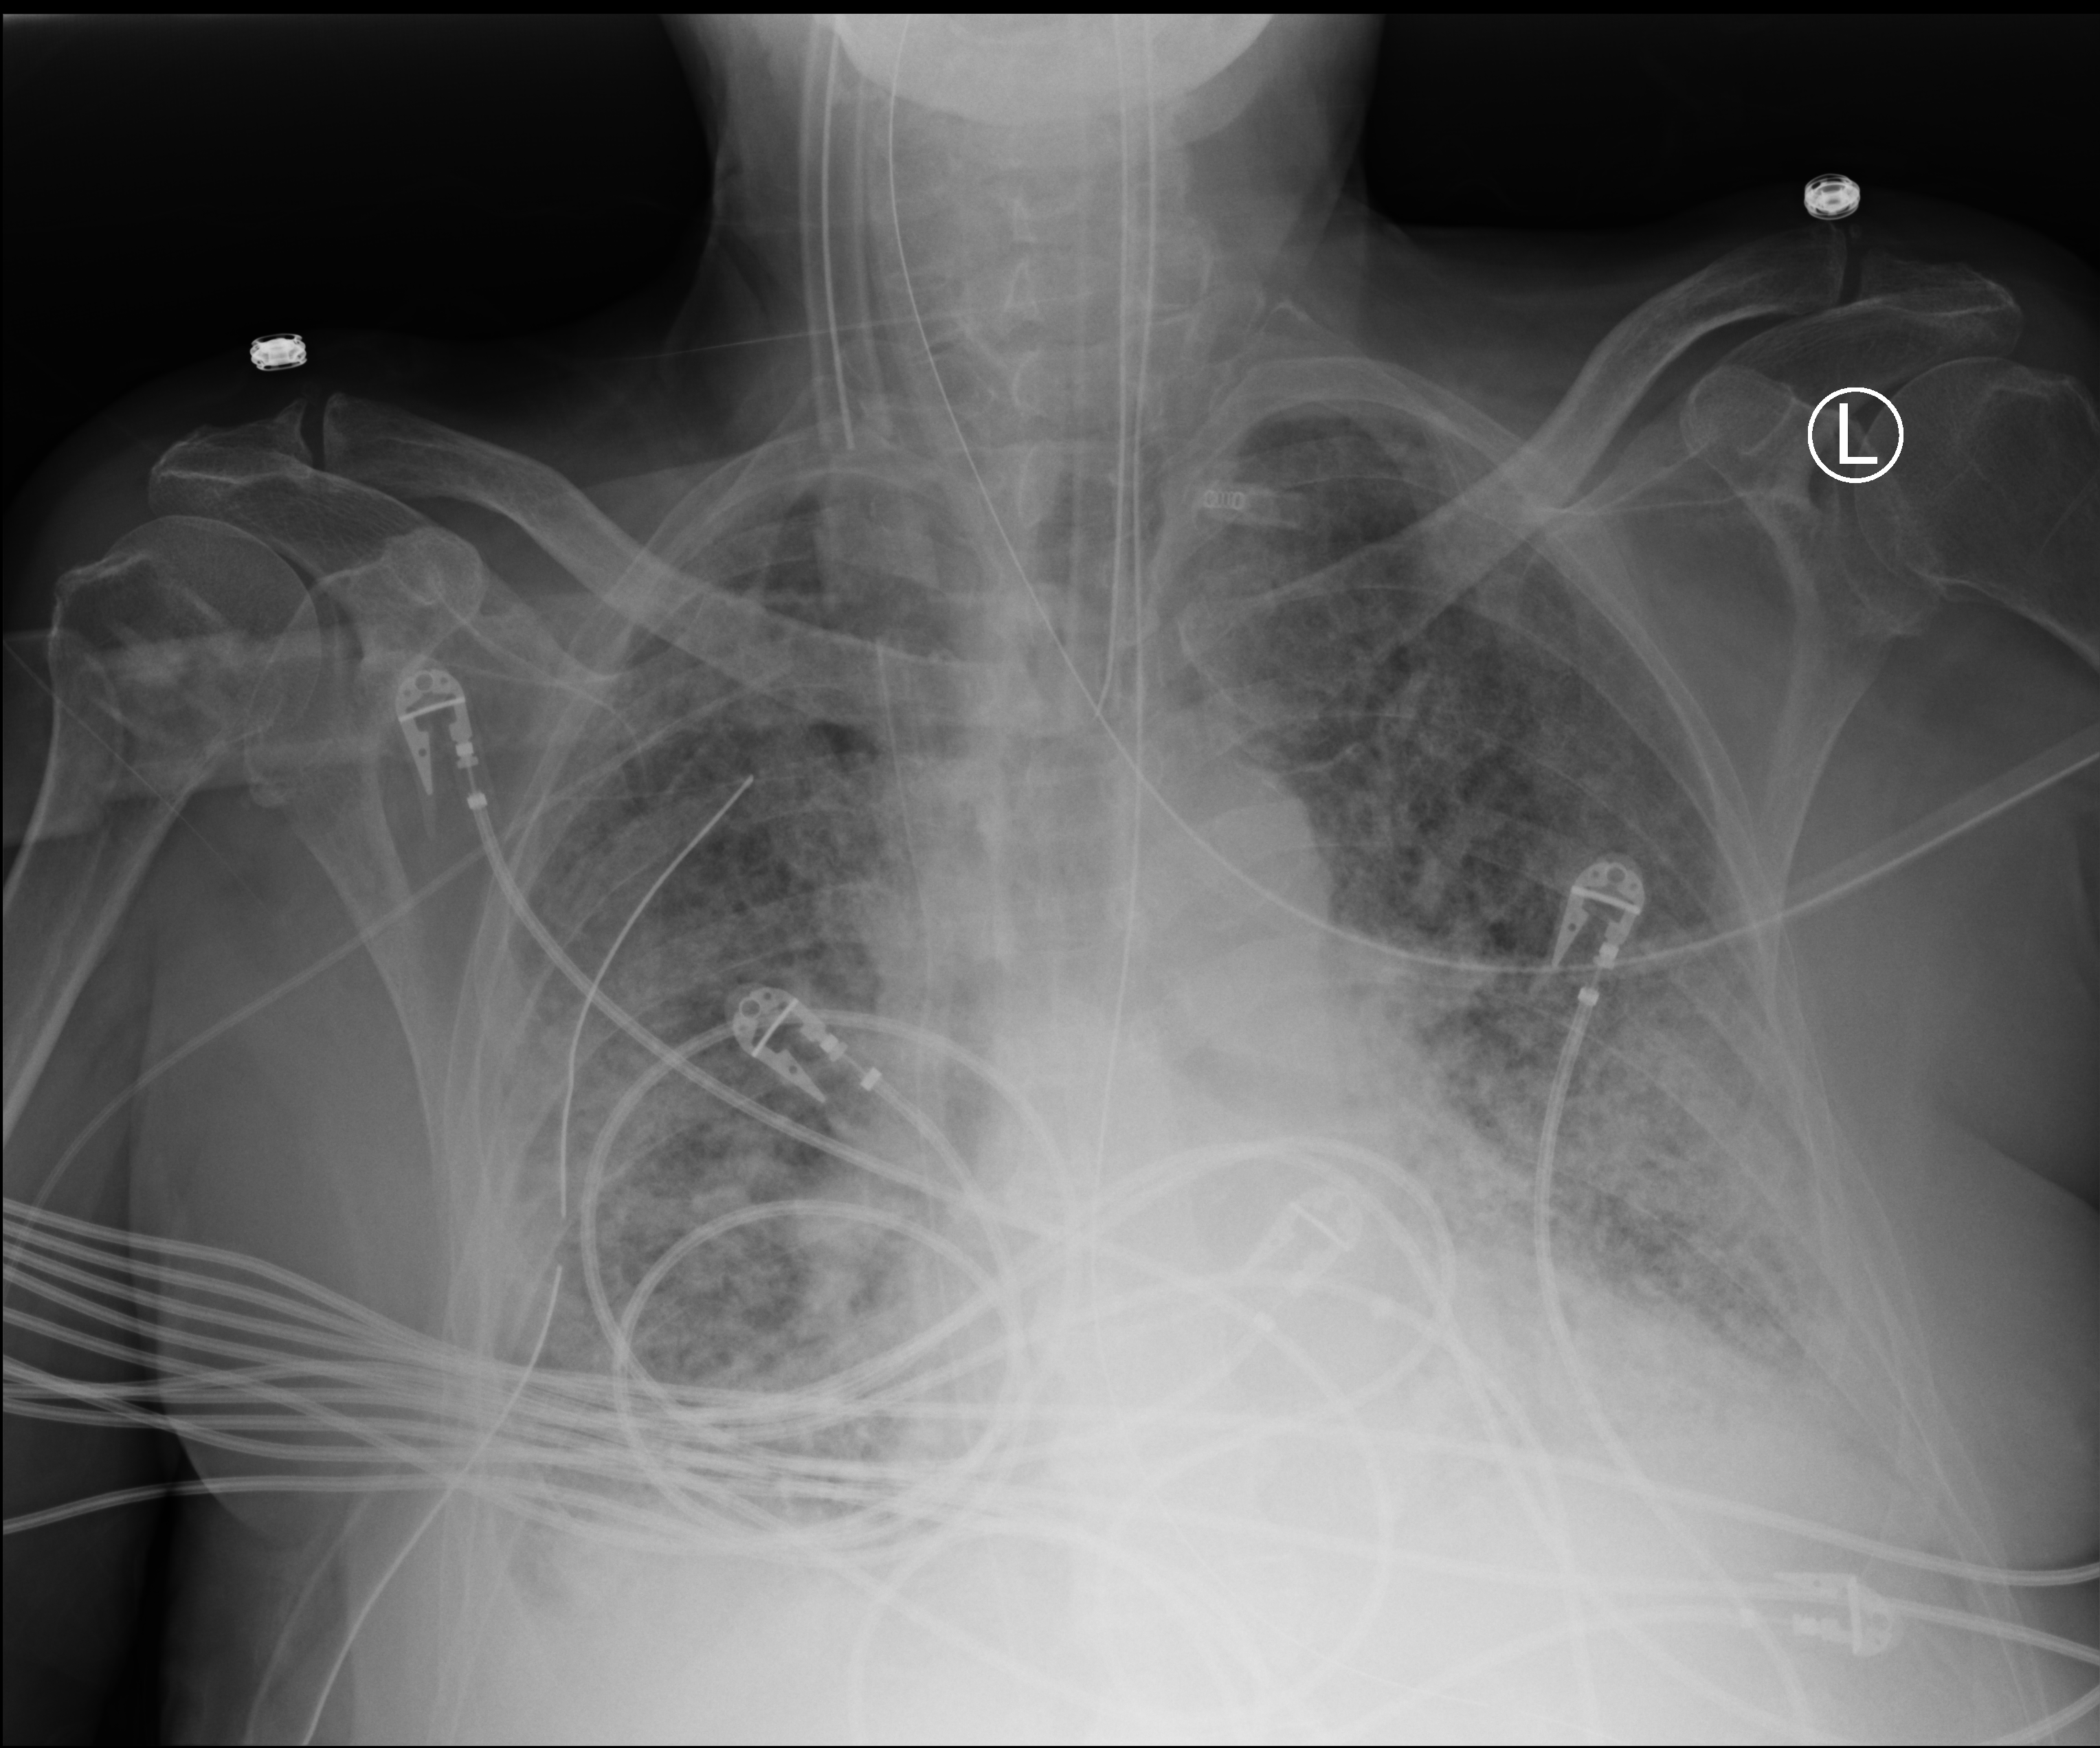
Bedside chest radiograph (computed radiography), anteroposterior (AP) projection. Patient hospitalised with COVID-19; male, aged 75–90 years.
From the hospital-stay record, not from the radiograph (when in the stay this image was taken is not recorded):
- admitted to intensive care during this hospital stay: yes
- hypertension (admission record): no
- mechanically ventilated during this hospital stay: yes